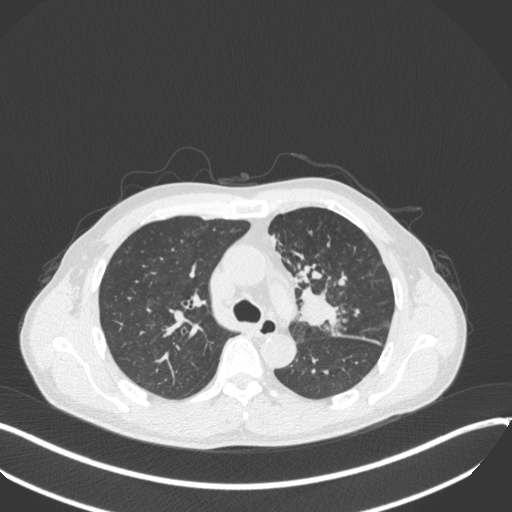
Chest CT, one axial slice; position 228 of 411 along the scan axis; lung window (W 1500 / L -600 HU); 1 mm slice thickness; 512 × 512 image matrix, field of view 400 × 400 mm. Patient: male, 56 years. Case-level facts recorded for this patient, not image findings: clinical TNM (as recorded): T2a N0 M0.
Structures marked on this image (bounding box drawn by a radiologist):
- lung tumour (recorded histology: squamous cell carcinoma): bounding box [x1, y1, x2, y2] px = [299, 282, 344, 332]